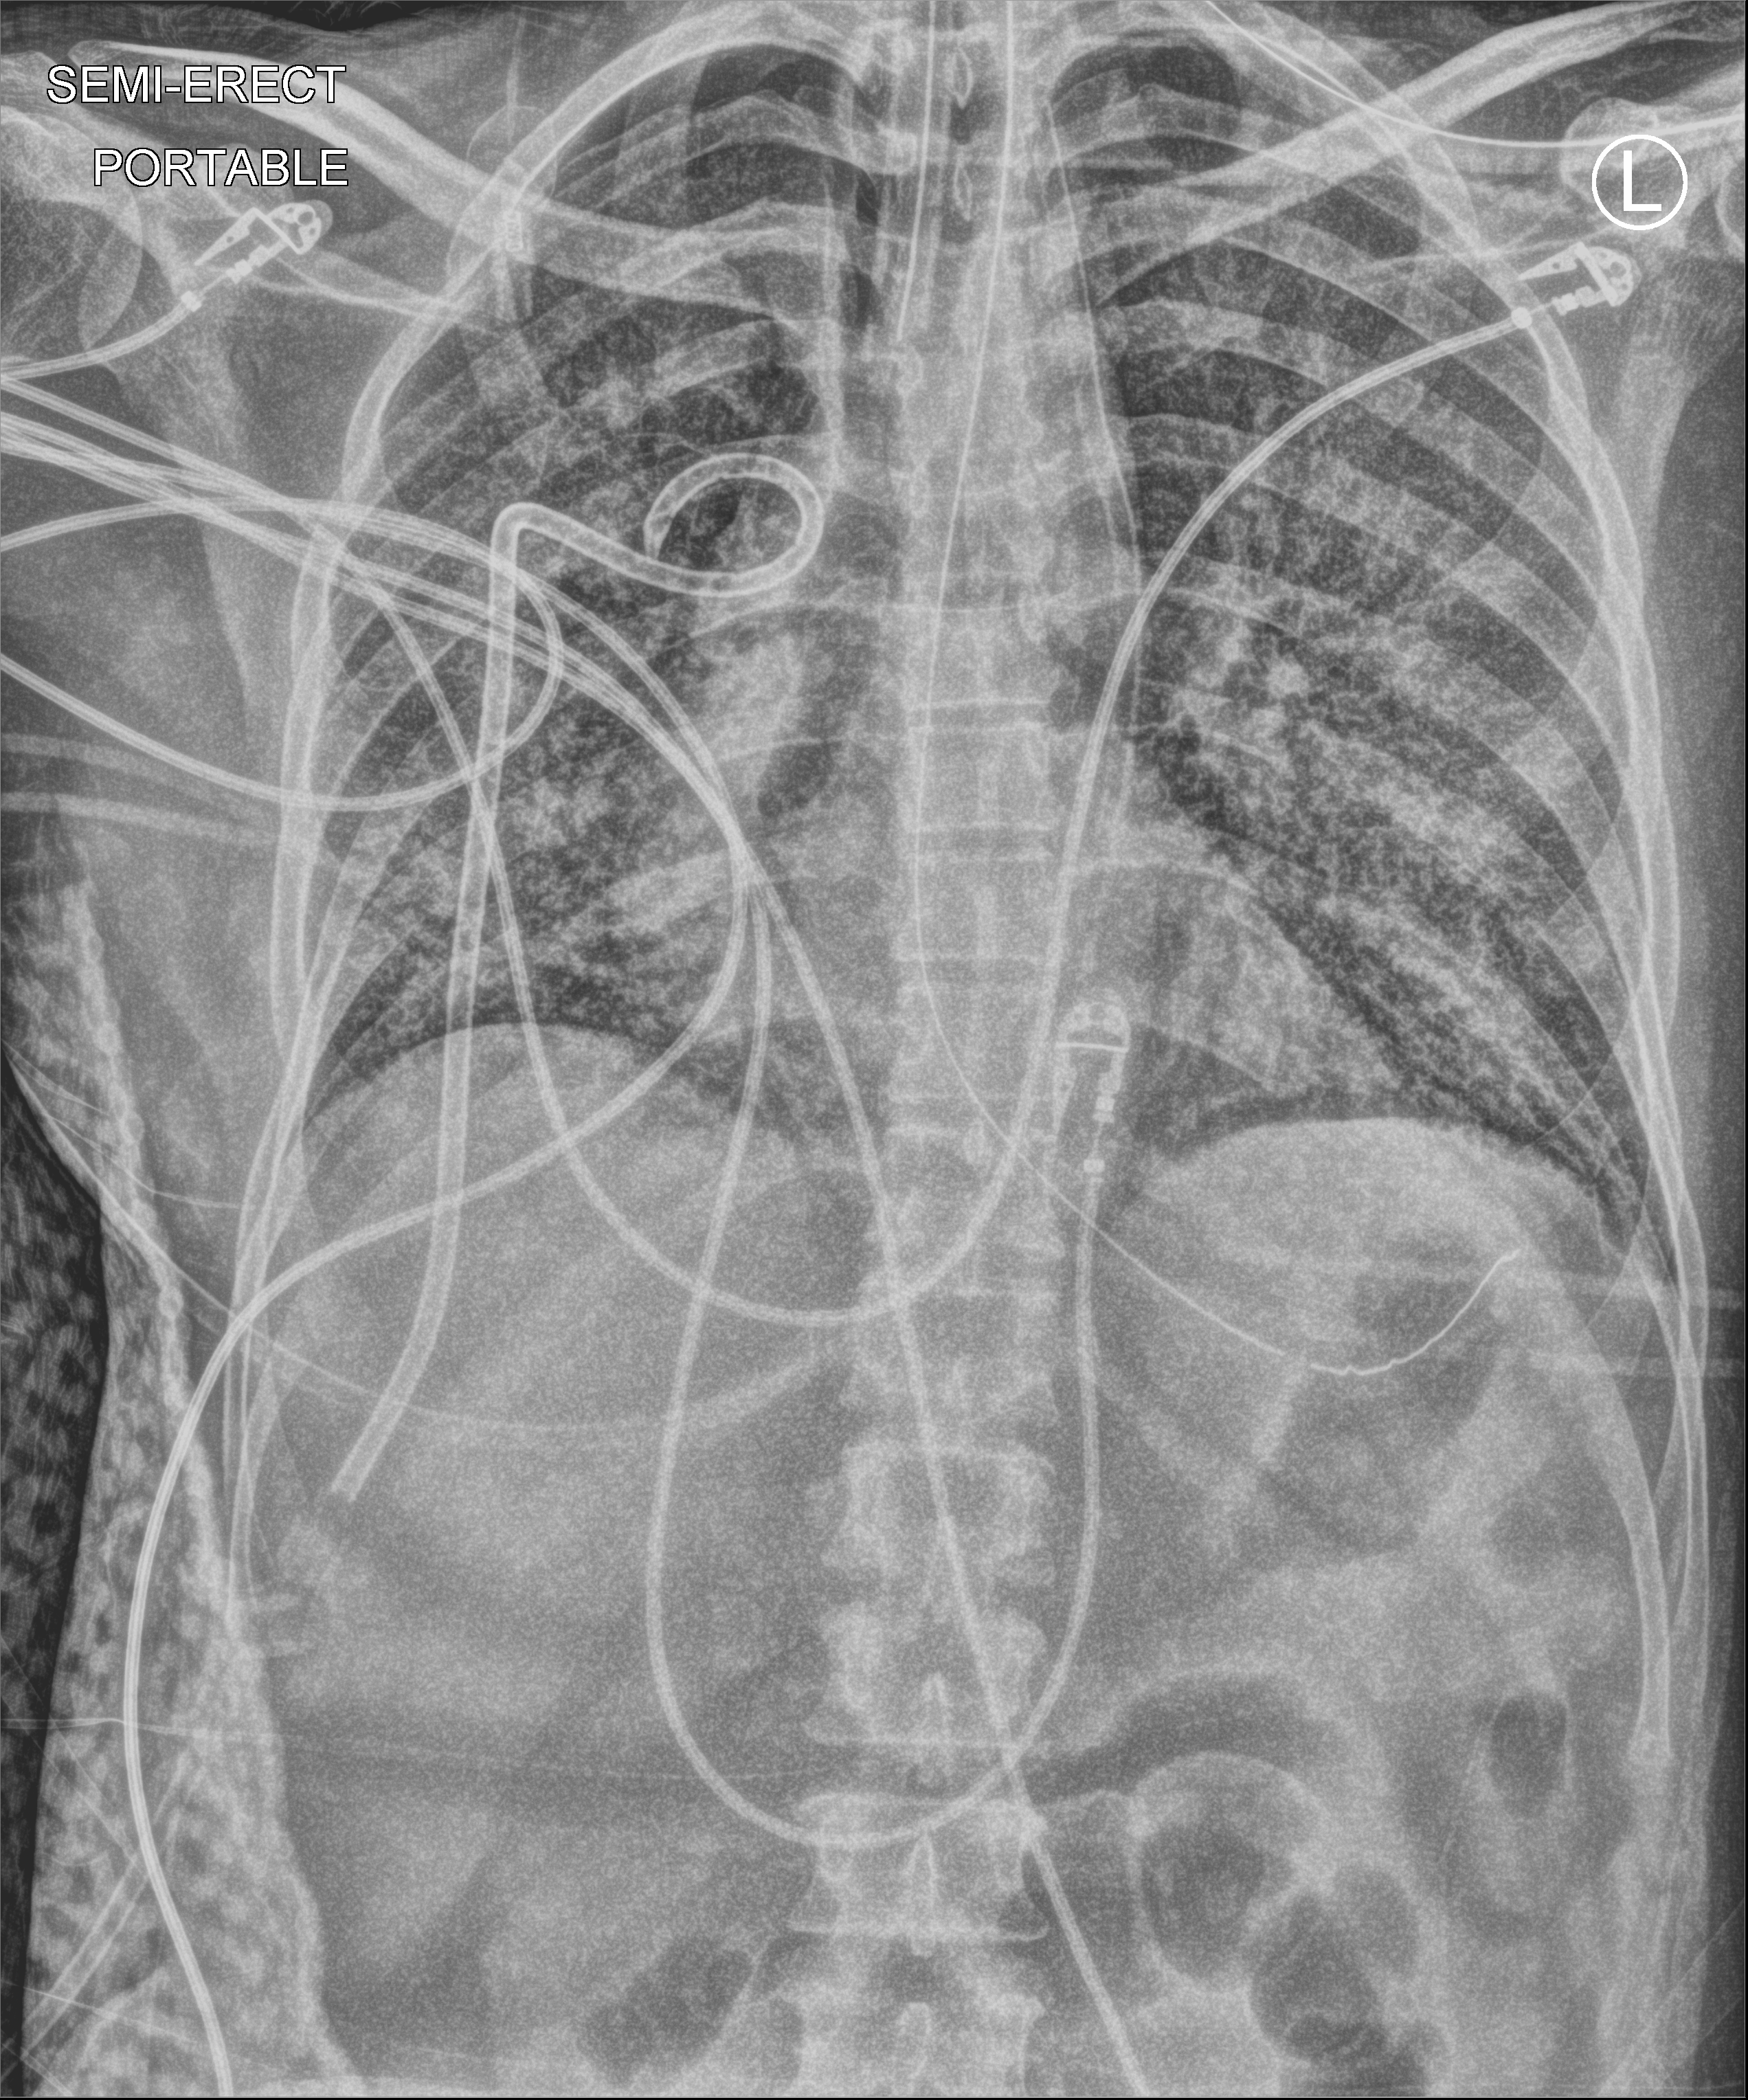
Bedside chest radiograph (computed radiography). Adult patient hospitalised with COVID-19, age 18–59 years.
Admission-level facts for this patient (not findings on this image; timing relative to this image not recorded):
- mechanically ventilated during this hospital stay: yes
- admitted to intensive care during this hospital stay: yes